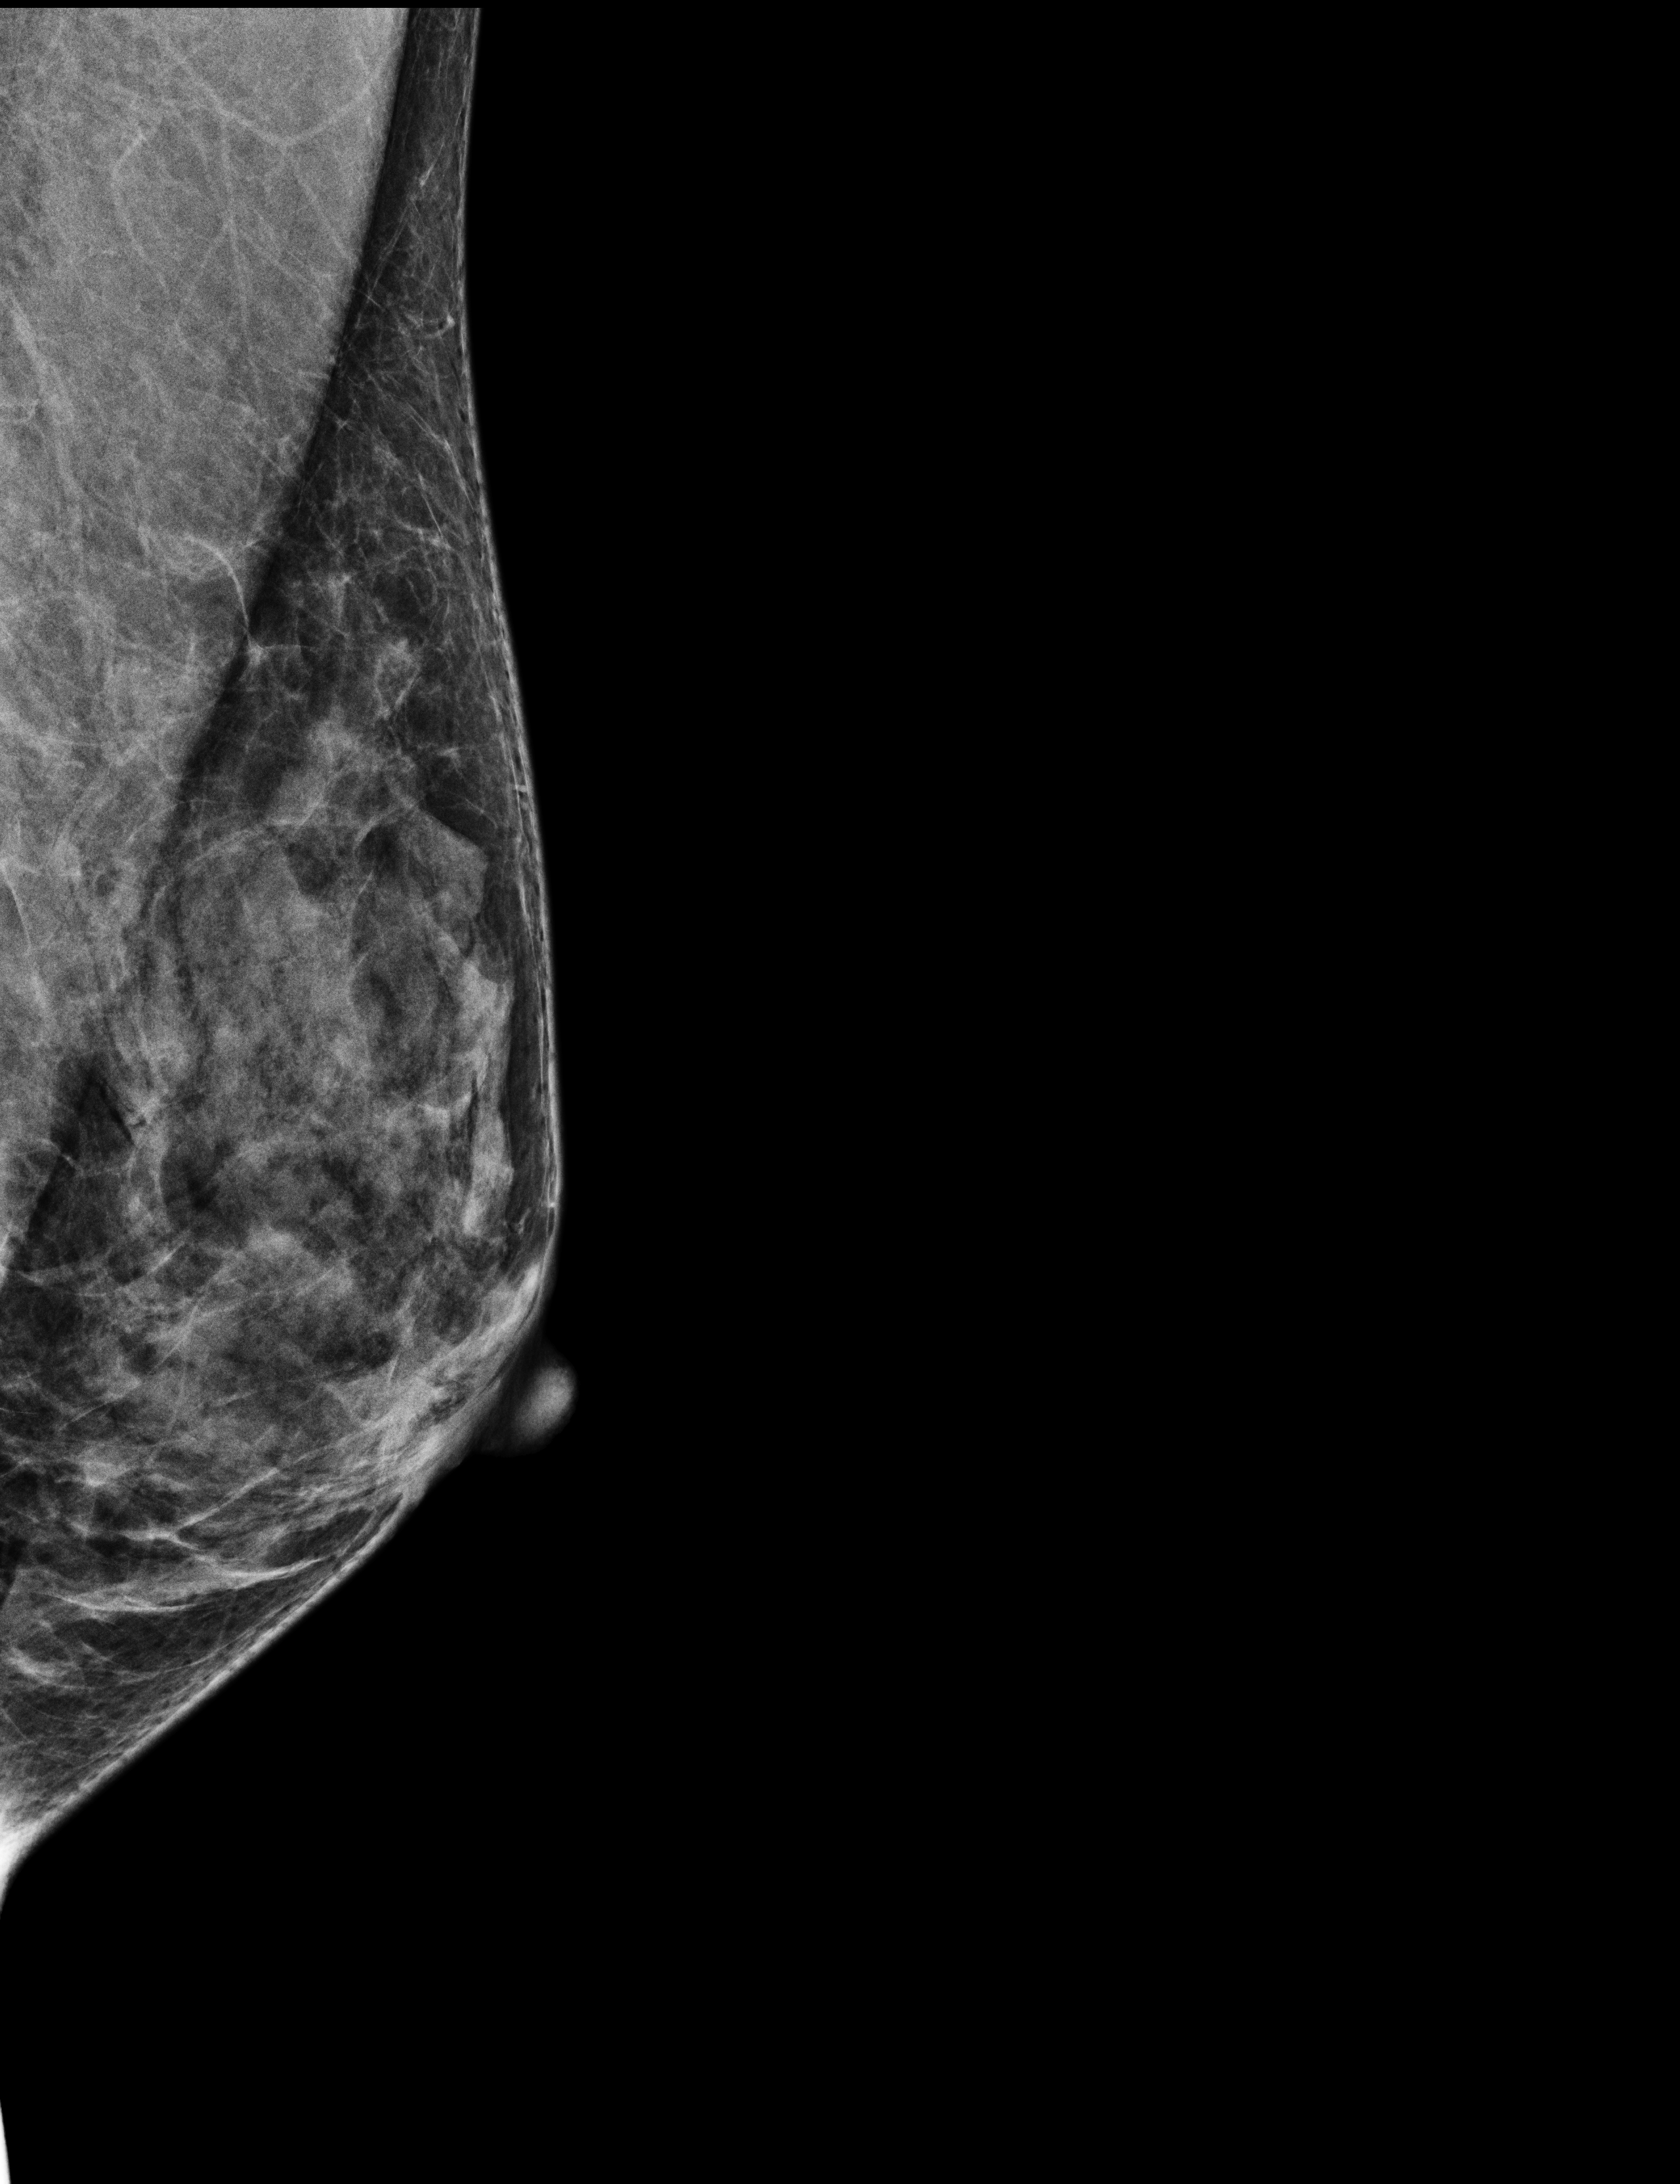
Digital mammogram (FFDM), left breast, MLO view, screening examination. Female patient, age 43 years.
- breast density at the screening exam (both breasts): heterogeneously dense (BI-RADS density category c)
- final BI-RADS assessment for this screening round (tomosynthesis exam, both breasts): category 2
- recall: no recall after this screen